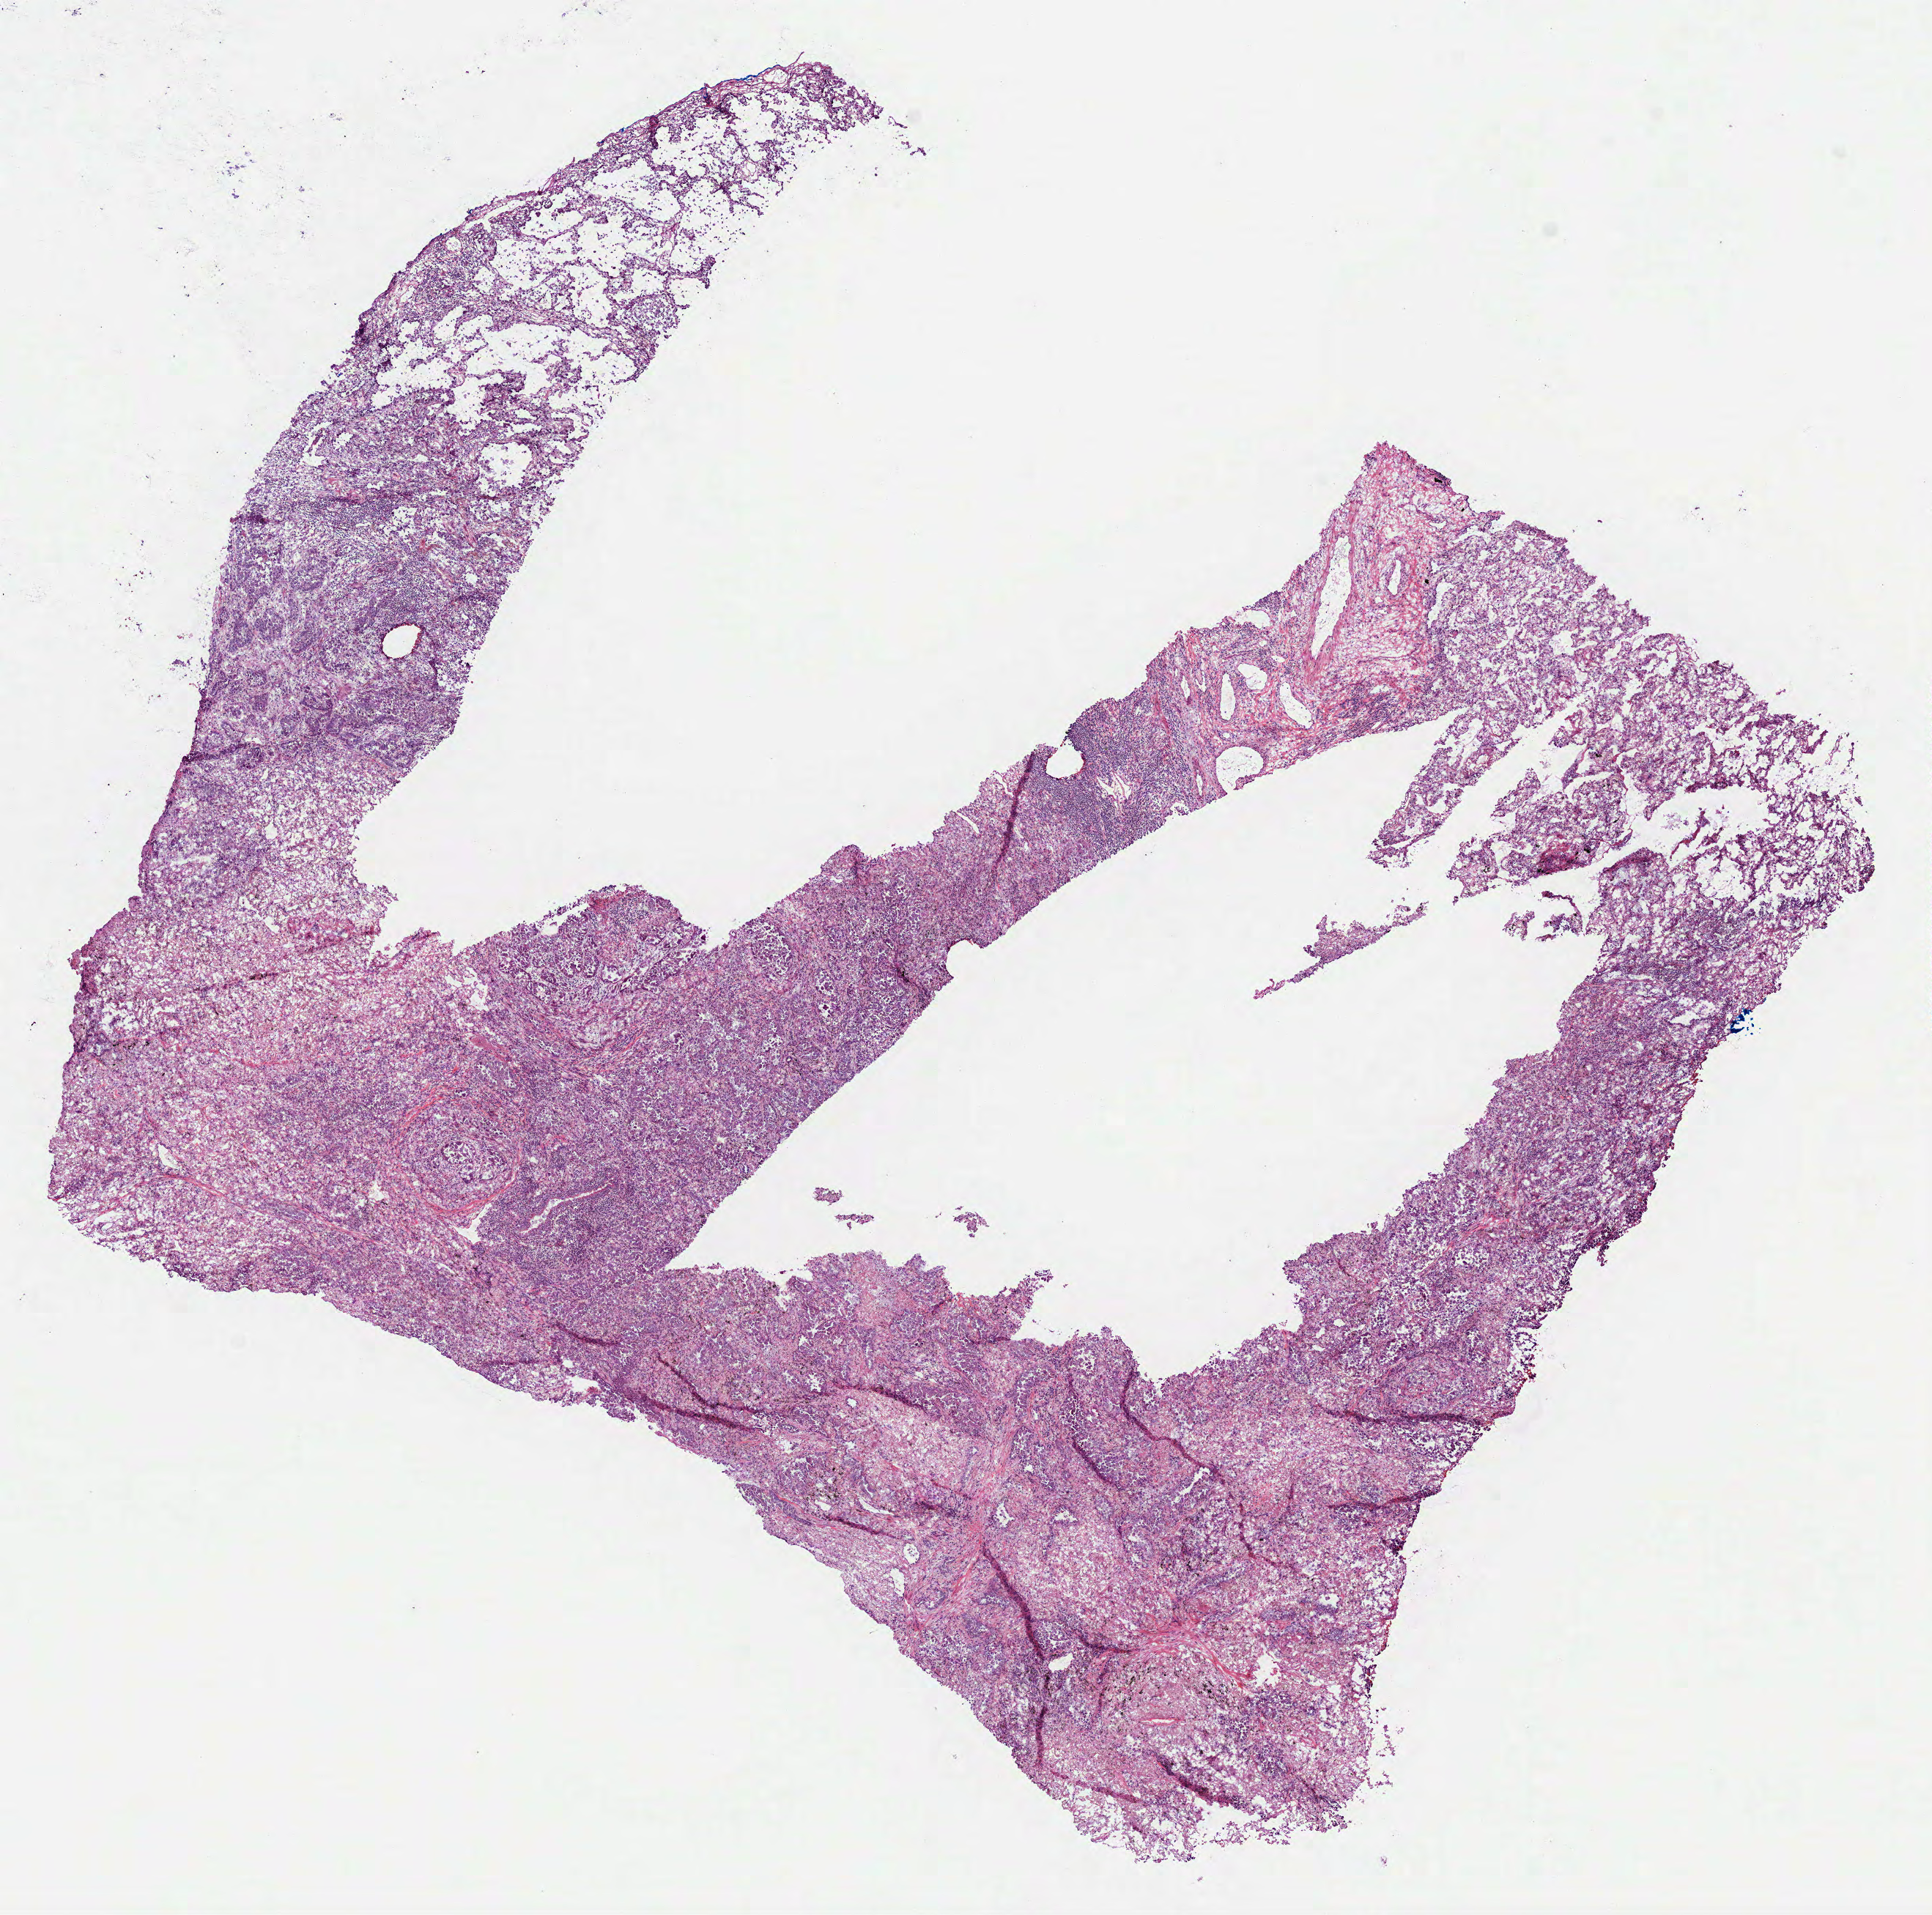
Hematoxylin and eosin (H&E) stained whole-slide image, whole scanned area (about 10.6 x 10.5 mm) shown as a low-resolution overview, frozen section from the bottom of the tissue portion, primary tumour sample from the lung. Patient: female, age at initial diagnosis 64 years. Slide review estimates, as recorded: tumour cells 72%, tumour nuclei 60%, normal cells 18%, stromal cells 10%, necrosis 0%.
TNM: T2a N0 M0. Laterality: right. AJCC pathologic stage: IB (7th edition). Pathologic diagnosis: Adenocarcinoma, NOS (upper lobe, lung).